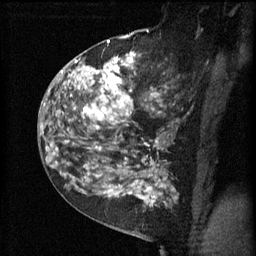
Breast MRI (dynamic contrast-enhanced), one sagittal slice. Position 33 of 60 along the scan axis. 3 images stored at this slice position (order not interpretable as contrast timing). 1.5 T. TE 4.2 ms, TR 11 ms. 2 mm slice thickness. 256 × 256 image matrix, field of view 180 × 180 mm. Female patient, age 52 years.
Structures marked on this image (semi-automatically segmented with operator editing):
- analysis volume of interest (the breast-tissue region the enhancement analysis was run in; not a lesion): bounding box [x1, y1, x2, y2] px = [81, 52, 174, 157]
- tumour enhancement mask (voxels above the 70 % enhancement threshold inside the analysis volume of interest): [81, 52, 163, 157]